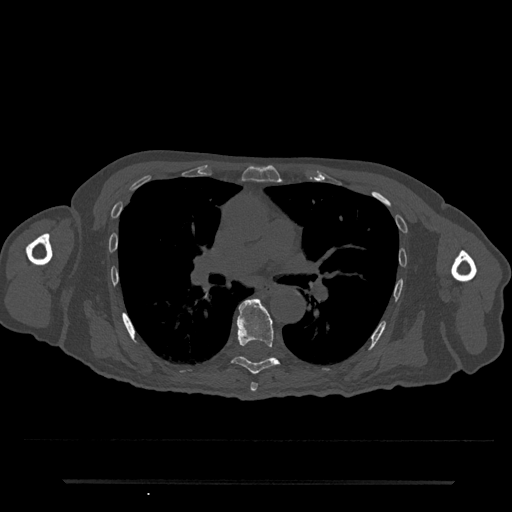
CT including the spine, one axial slice; slice 480 of 797 in the series (ordered by position); bone window (W 1800 / L 400 HU); 0.5 mm slice thickness; 512 × 512 image matrix. Patient: male, 74 years. Case-level facts recorded for this patient, not image findings: primary cancer: prostate.
Outlined on this slice (semi-automatic segmentation, software-assisted and operator-edited):
- T6 vertebra: bounding box [x1, y1, x2, y2] px = [250, 383, 258, 392]
- T7 vertebra: [232, 299, 280, 375]